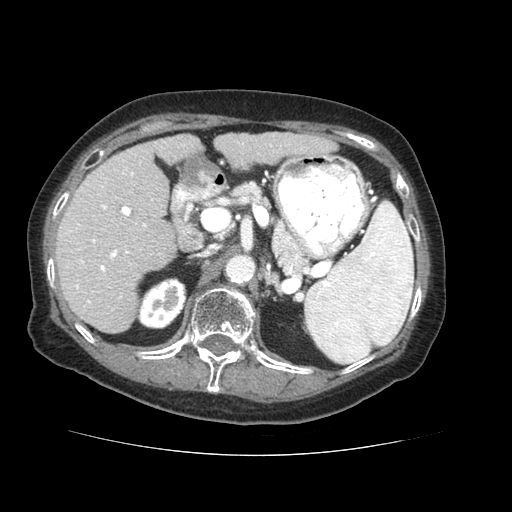
Contrast-enhanced abdominal CT (liver protocol), one axial slice; slice 29 of 73 in the series (ordered by position); reconstruction kernel STANDARD; 120 kVp; soft-tissue window (W 400 / L 40 HU); 2.5 mm slice thickness; 512 × 512 image matrix, field of view 360 × 360 mm. Case-level facts recorded for this patient, not image findings: diagnosis: hepatocellular carcinoma (patient treated with transarterial chemoembolisation; whether this scan precedes or follows treatment is not stated here); TNM stage (as recorded): Stage-IVB; Child-Pugh class: A; tumour differentiation: well differentiated; tumour nodularity: uninodular.
Outlined on this slice (semi-automatic segmentation, software-assisted and operator-edited):
- liver parenchyma outside the tumour (the mass and vessels are separate outlines, so this box may not span the whole liver): bounding box [x1, y1, x2, y2] px = [54, 132, 330, 332]
- liver vessels: [70, 144, 272, 303]